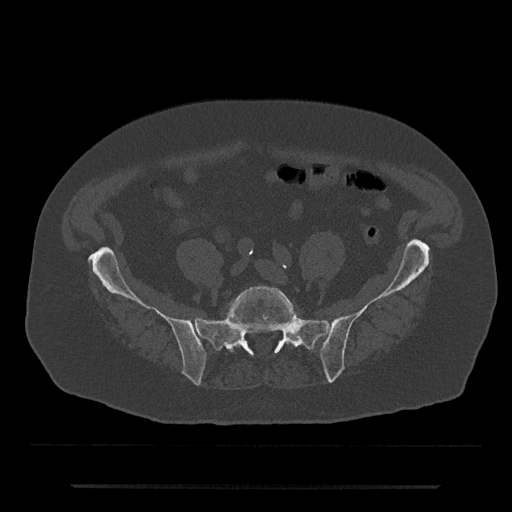
CT including the spine, one axial slice. Slice 255 of 797 in the series (ordered by position). 120 kVp. Bone window (W 1800 / L 400 HU). 0.5 mm slice thickness. 512 × 512 image matrix, field of view 434 × 434 mm. Patient: male, 80 years. From the clinical record (not read from this slice): primary cancer: prostate; vertebrae with lytic lesions (as recorded): L1, T11.
Outlined on this slice (semi-automatically segmented with operator editing):
- L5 vertebra: box from (x=226, y=286) to (x=299, y=352) px